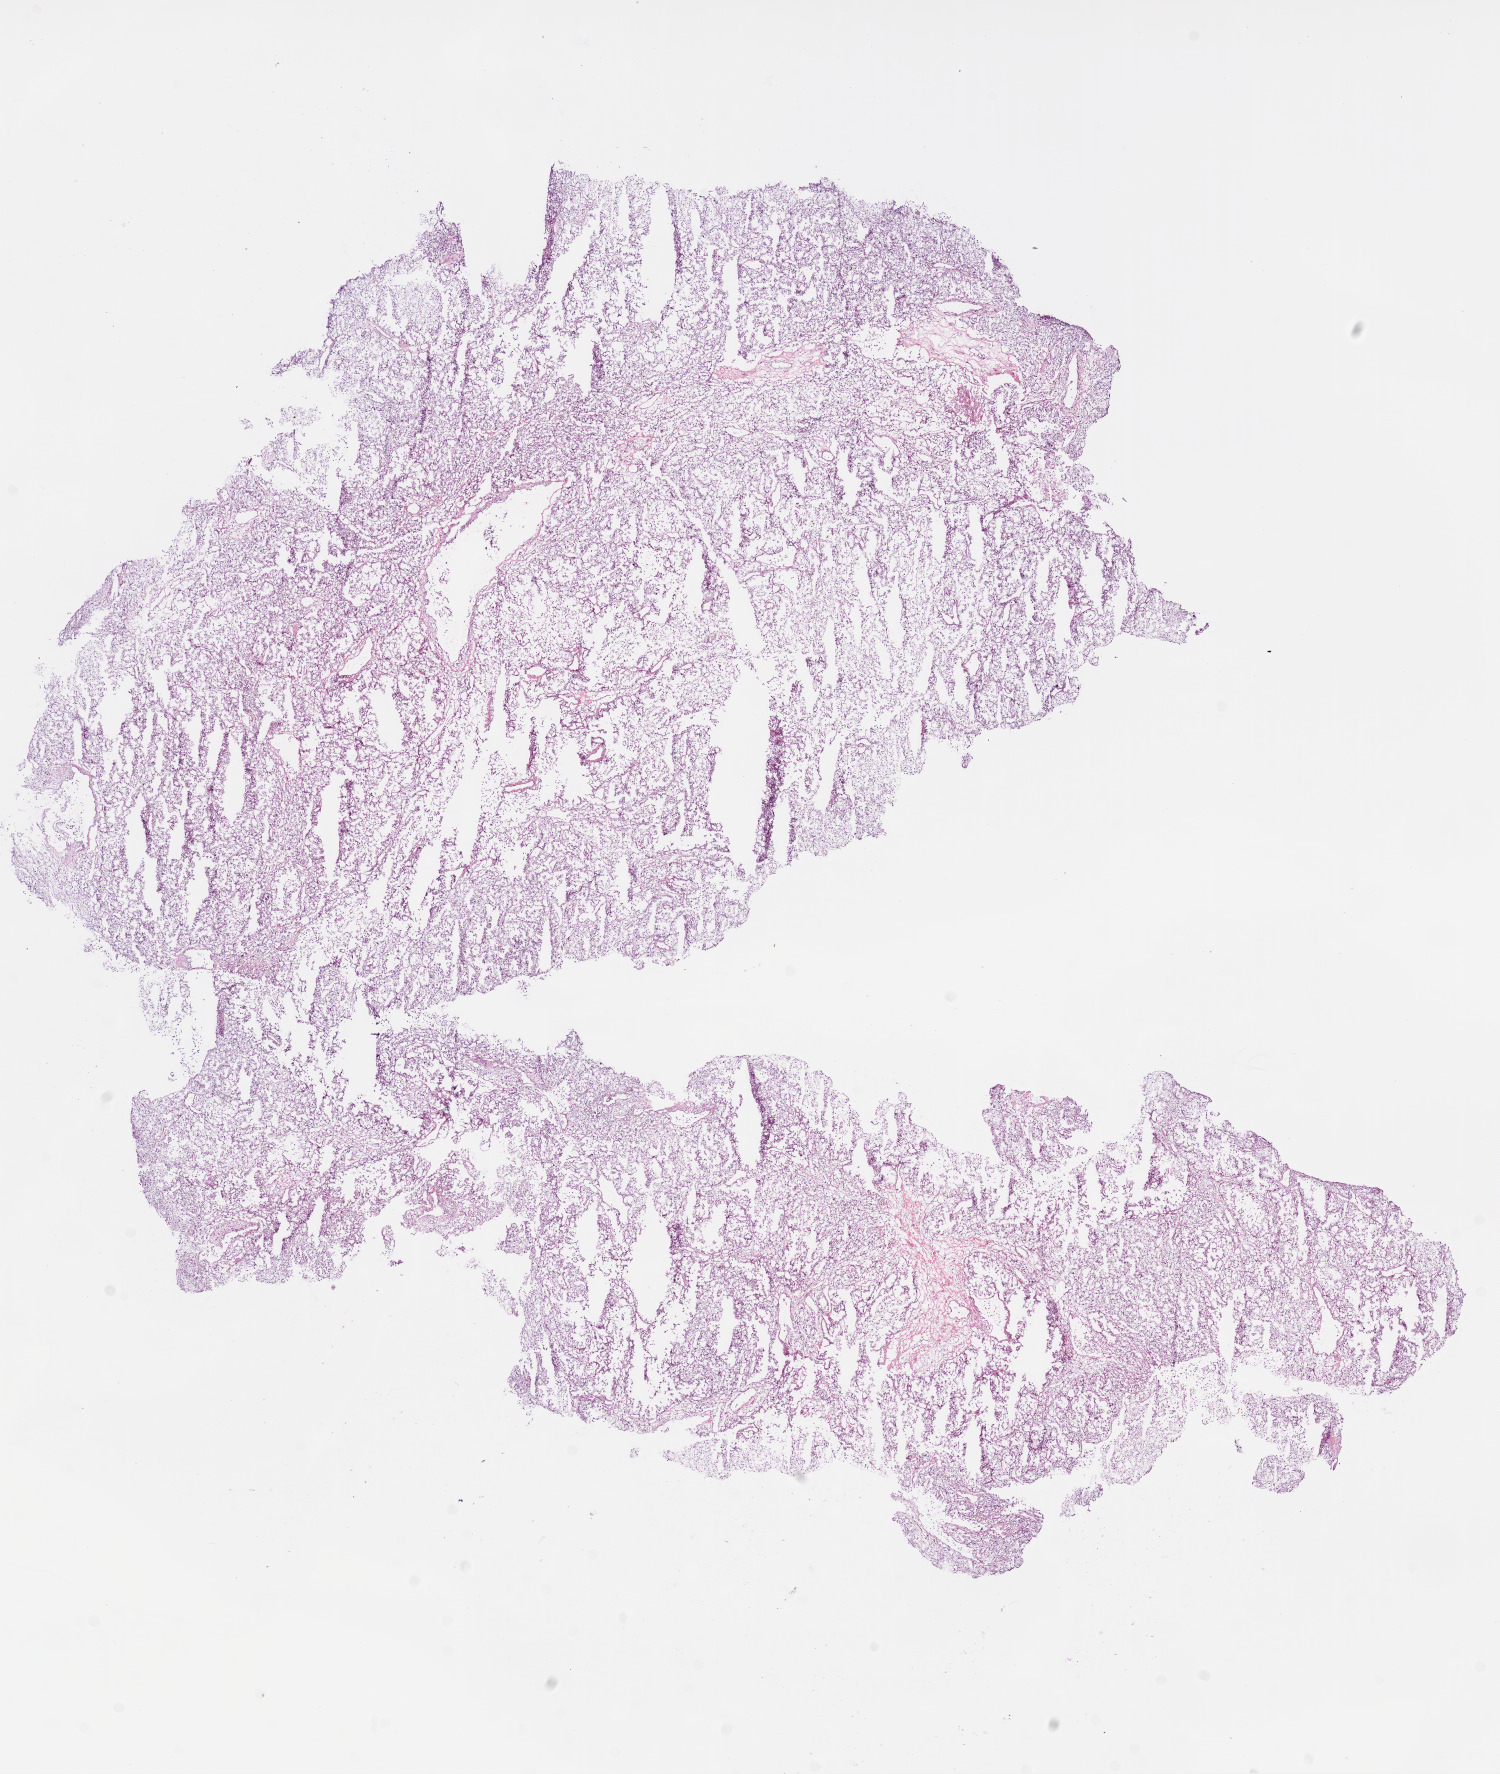
Hematoxylin and eosin (H&E) stained whole-slide image — low-resolution overview of the scanned area, about 12.0 x 14.2 mm (acquisition: 20x scan); frozen section; primary tumour sample from the kidney. Male patient; age at initial diagnosis 52 years. Histologic grade: G3 (poorly differentiated). Pathologist review of this section (percent, as recorded): tumour cells 90%, tumour nuclei 85%, normal cells 0%, stromal cells 10%, necrosis 0%.
* laterality: left
* AJCC pathologic stage: I
* histologic diagnosis: Clear cell adenocarcinoma, NOS